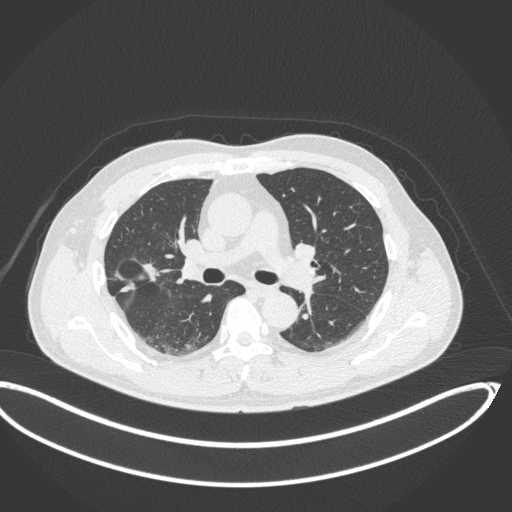
Chest CT, one axial slice; reconstruction kernel B31f; 120 kVp; lung window (W 1500 / L -600 HU); 1 mm slice thickness; 512 × 512 image matrix, field of view 439 × 439 mm. Male patient, age 63 years. From the clinical record (not read from this slice): clinical TNM (as recorded): T1c N0 M0.
Annotated regions visible in this slice (bounding box drawn by a radiologist):
- lung tumour (recorded histology: adenocarcinoma): bounding box <112,251,162,299> (left, top, right, bottom; pixels)